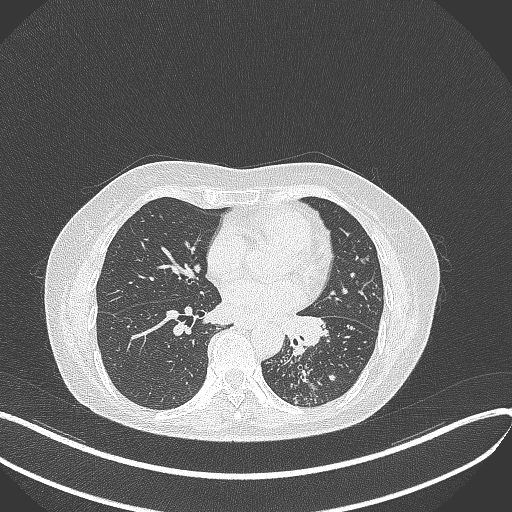
Chest CT, one axial slice; slice 185 of 429 in the series (ordered by position); reconstruction kernel B70f; lung window (W 1500 / L -600 HU); 1 mm slice thickness; 512 × 512 image matrix, field of view 400 × 400 mm. Patient: female, 63 years. From the clinical record (not read from this slice): clinical TNM (as recorded): T1b N0 M0; histopathological grade: G2-3.
Outlined on this slice (bounding box drawn by a radiologist):
- lung tumour (recorded histology: adenocarcinoma): bounding box <279,305,336,361> (left, top, right, bottom; pixels)